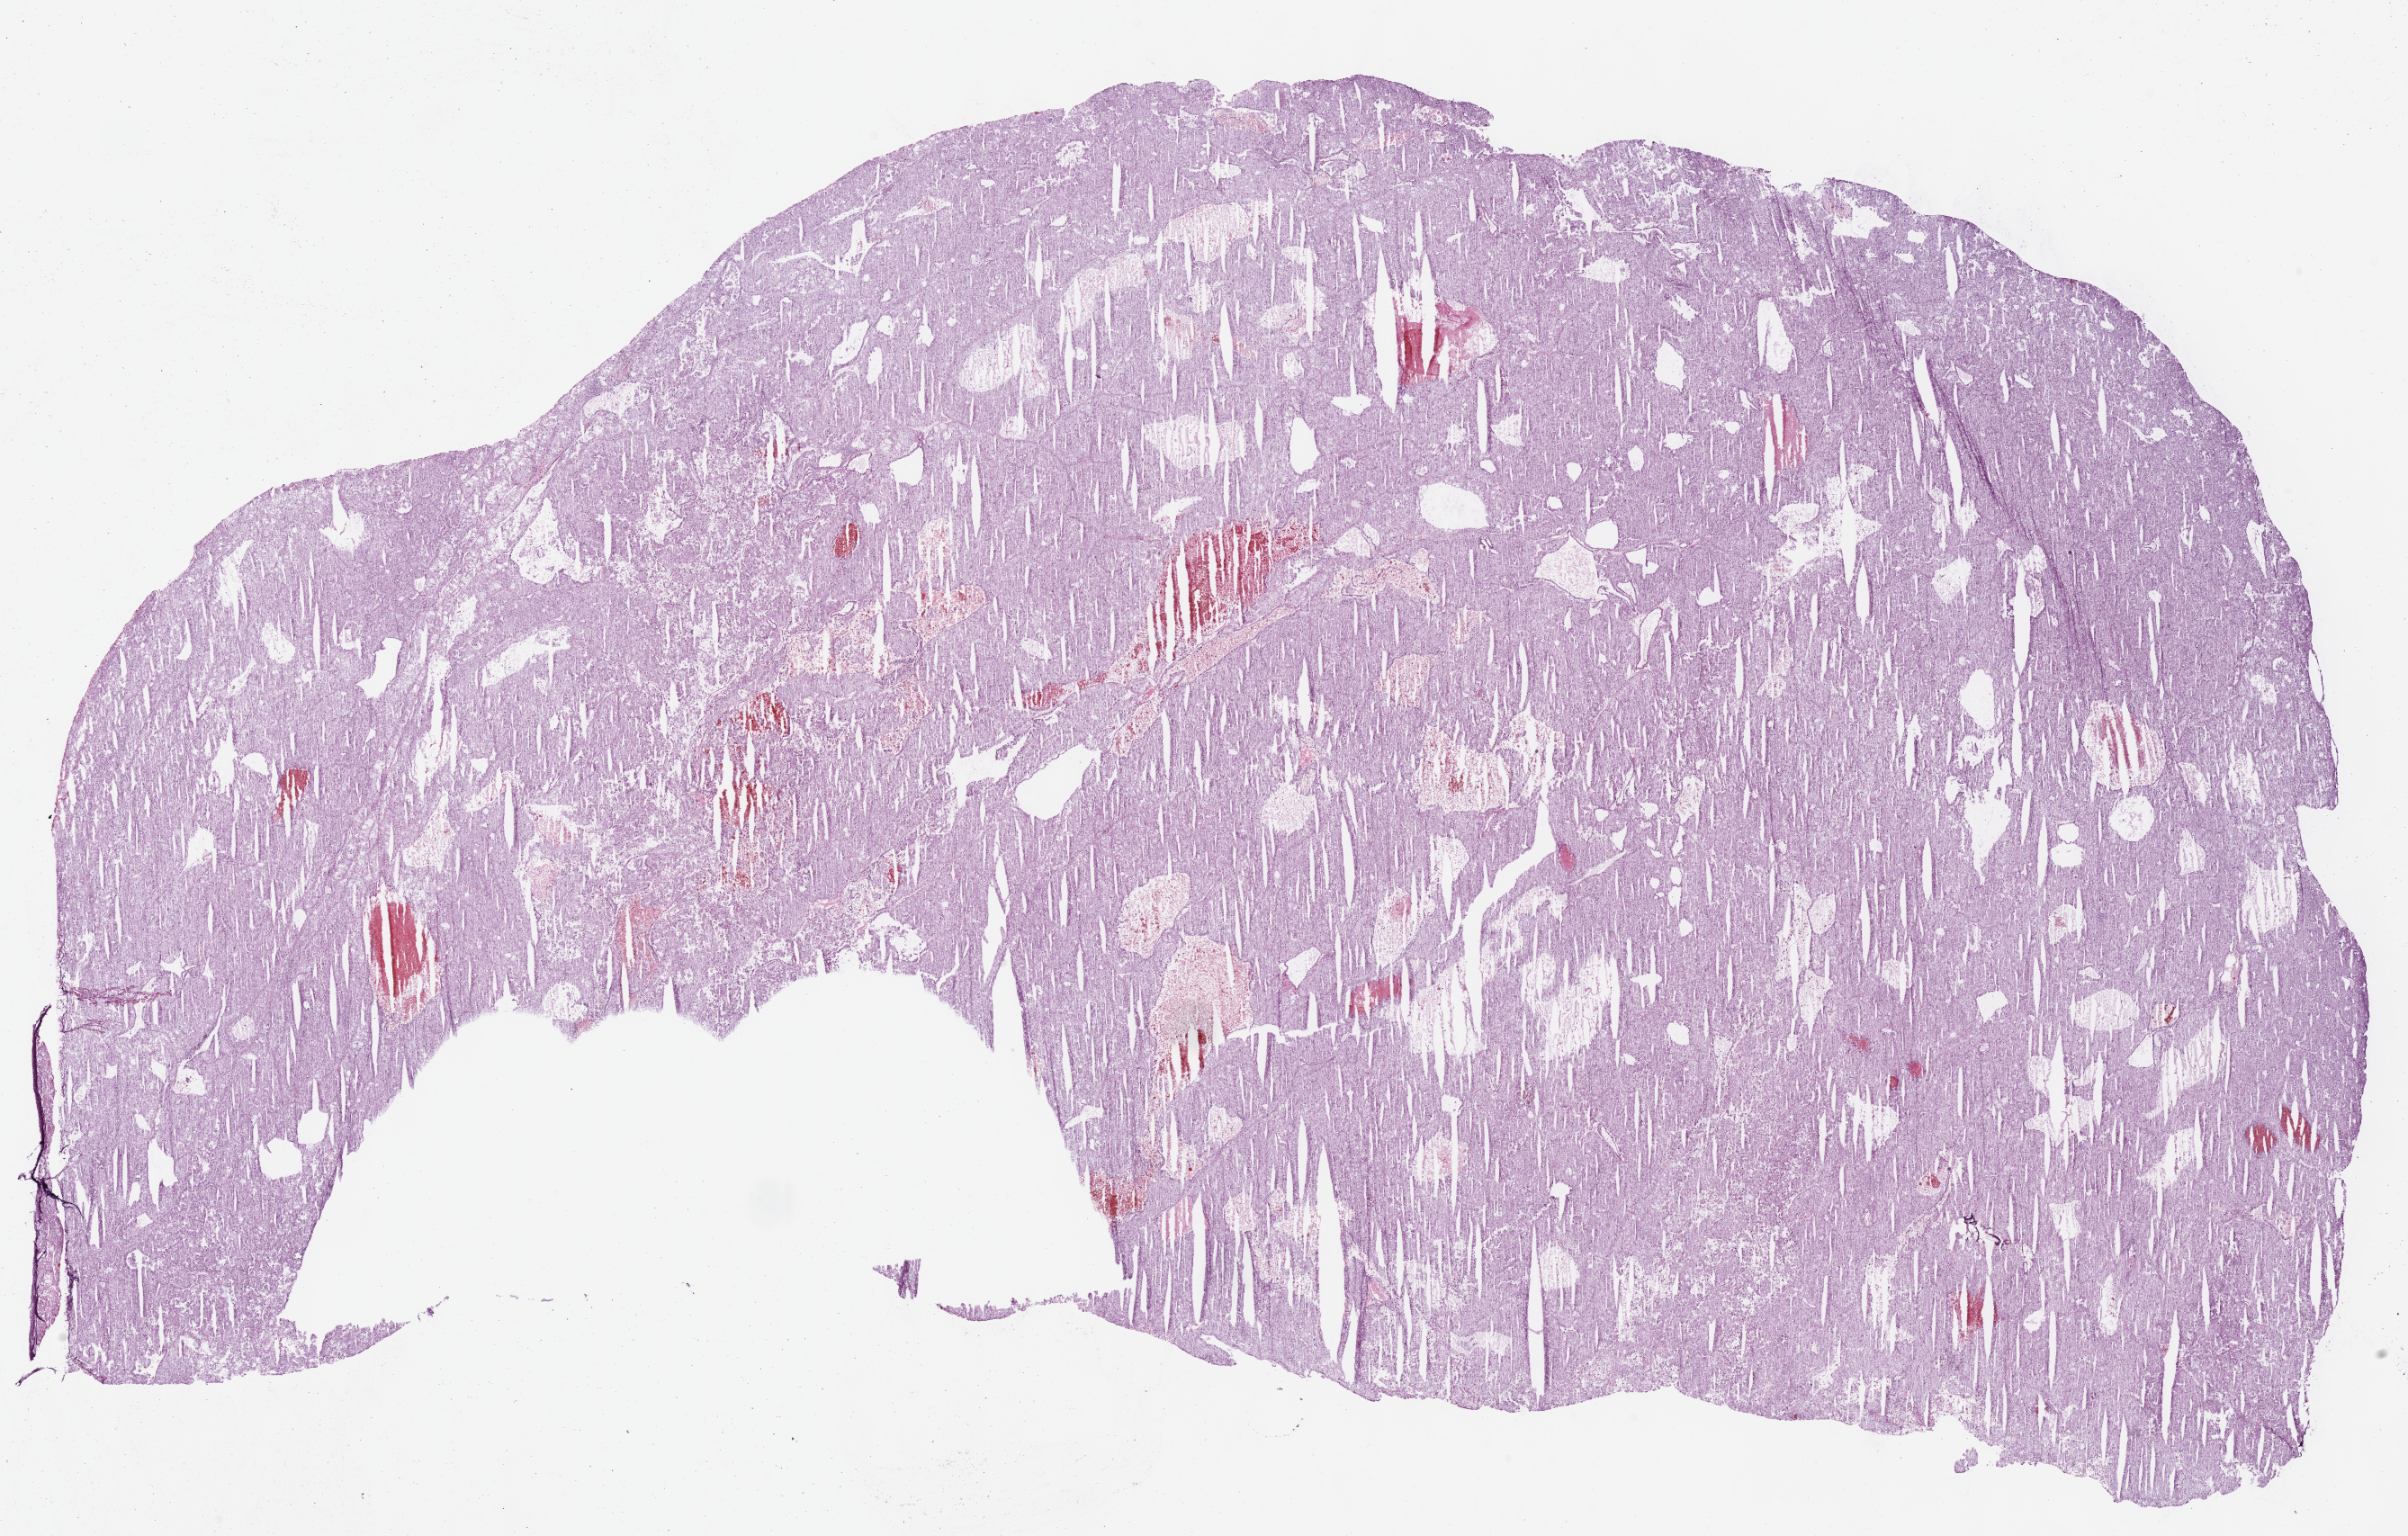
Digitized Hematoxylin and eosin (H&E) stained tissue section (whole slide), low-resolution overview of the scanned area, about 21.0 x 13.4 mm (from a 40x scan). Frozen section. Kidney, primary tumour sample. Male, age 75 years at initial diagnosis. Slide review estimates, as recorded: tumour cells 90%, tumour nuclei 90%.
Pathologic diagnosis: Renal cell carcinoma, chromophobe type.